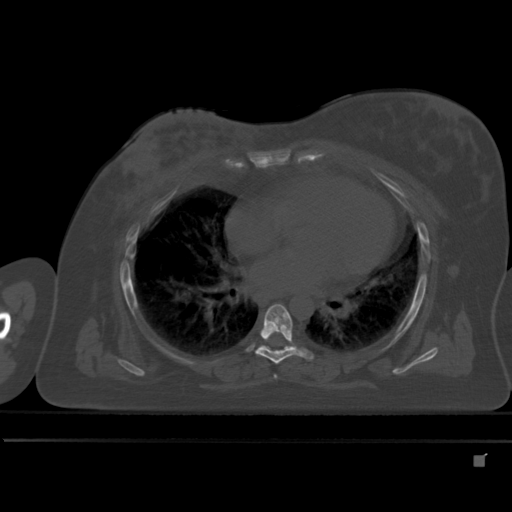
CT including the spine, one axial slice; bone window (W 1800 / L 400 HU); 1.5 mm slice thickness; 512 × 512 image matrix, field of view 404 × 404 mm. Patient: female, 33 years. Case-level facts recorded for this patient, not image findings: primary cancer: breast; vertebrae with lytic lesions (as recorded): T1.
Structures marked on this image (semi-automatic segmentation, software-assisted and operator-edited):
- T6 vertebra: box from (x=254, y=304) to (x=311, y=364) px
- T7 vertebra: (x=258, y=345)–(x=264, y=348)